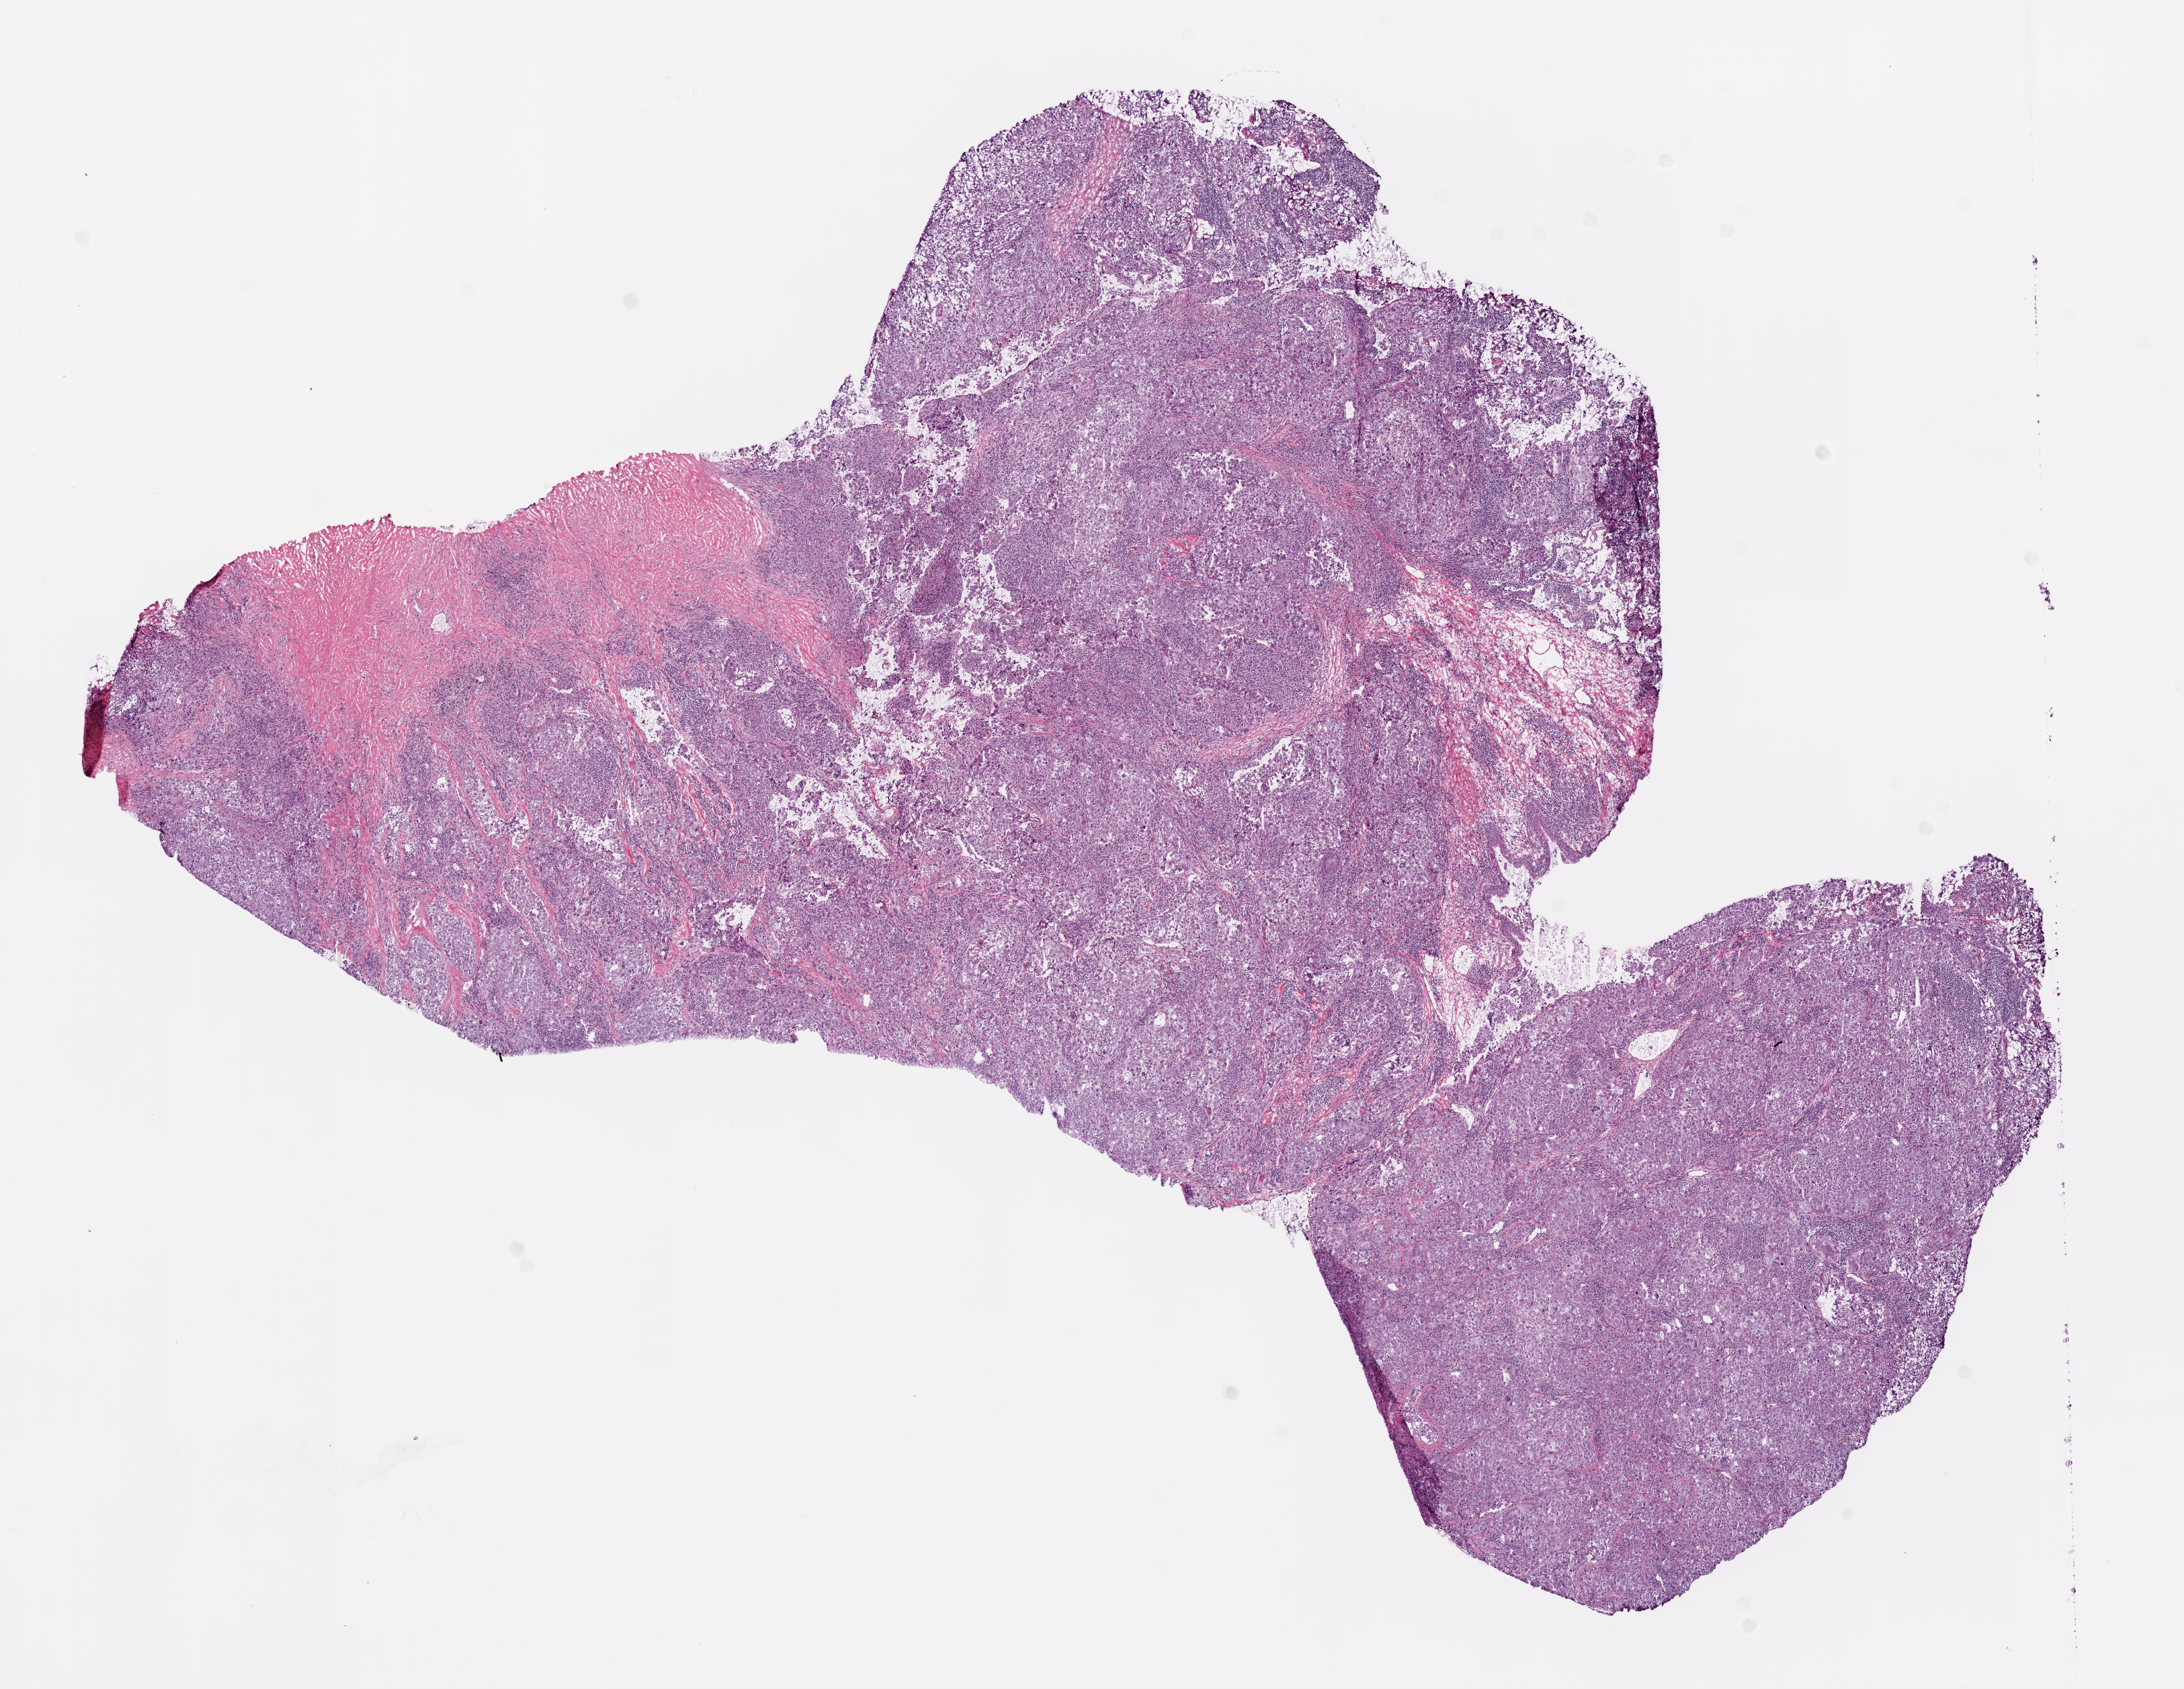
Digitized Hematoxylin and eosin (H&E) stained tissue section (whole slide), low-resolution overview of the scanned area, about 13.0 x 10.1 mm, frozen section from the bottom of the tissue portion, sample: primary tumour, lung. Male, age 78 years at initial diagnosis. Pathologist review of this section (percent, as recorded): tumour cells 92%, tumour nuclei 65%, normal cells 0%, stromal cells 8%, necrosis 0%. Infiltration values recorded for this section: lymphocyte infiltration 30%, monocyte infiltration 1%.
- pathologic diagnosis: Squamous cell carcinoma, NOS (upper lobe, lung)
- AJCC pathologic stage: IIA (7th edition)